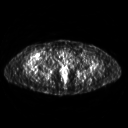
FDG PET of an extremity soft-tissue mass (from a PET/CT study), one axial slice; position 283 of 311 along the scan axis; 3.27 mm slice thickness; 128 × 128 image matrix, field of view 500 × 500 mm. Female patient, age 57 years. Case-level facts recorded for this patient, not image findings: histological type: pleiomorphic undifferentiated sarcoma; grade: high; site of the primary tumour: right quadricep.
Annotated regions visible in this slice (expert contour drawn on MRI and transferred to this co-registered scan by the dataset authors):
- tumour plus oedema (research contour): box from (x=25, y=52) to (x=41, y=69) px